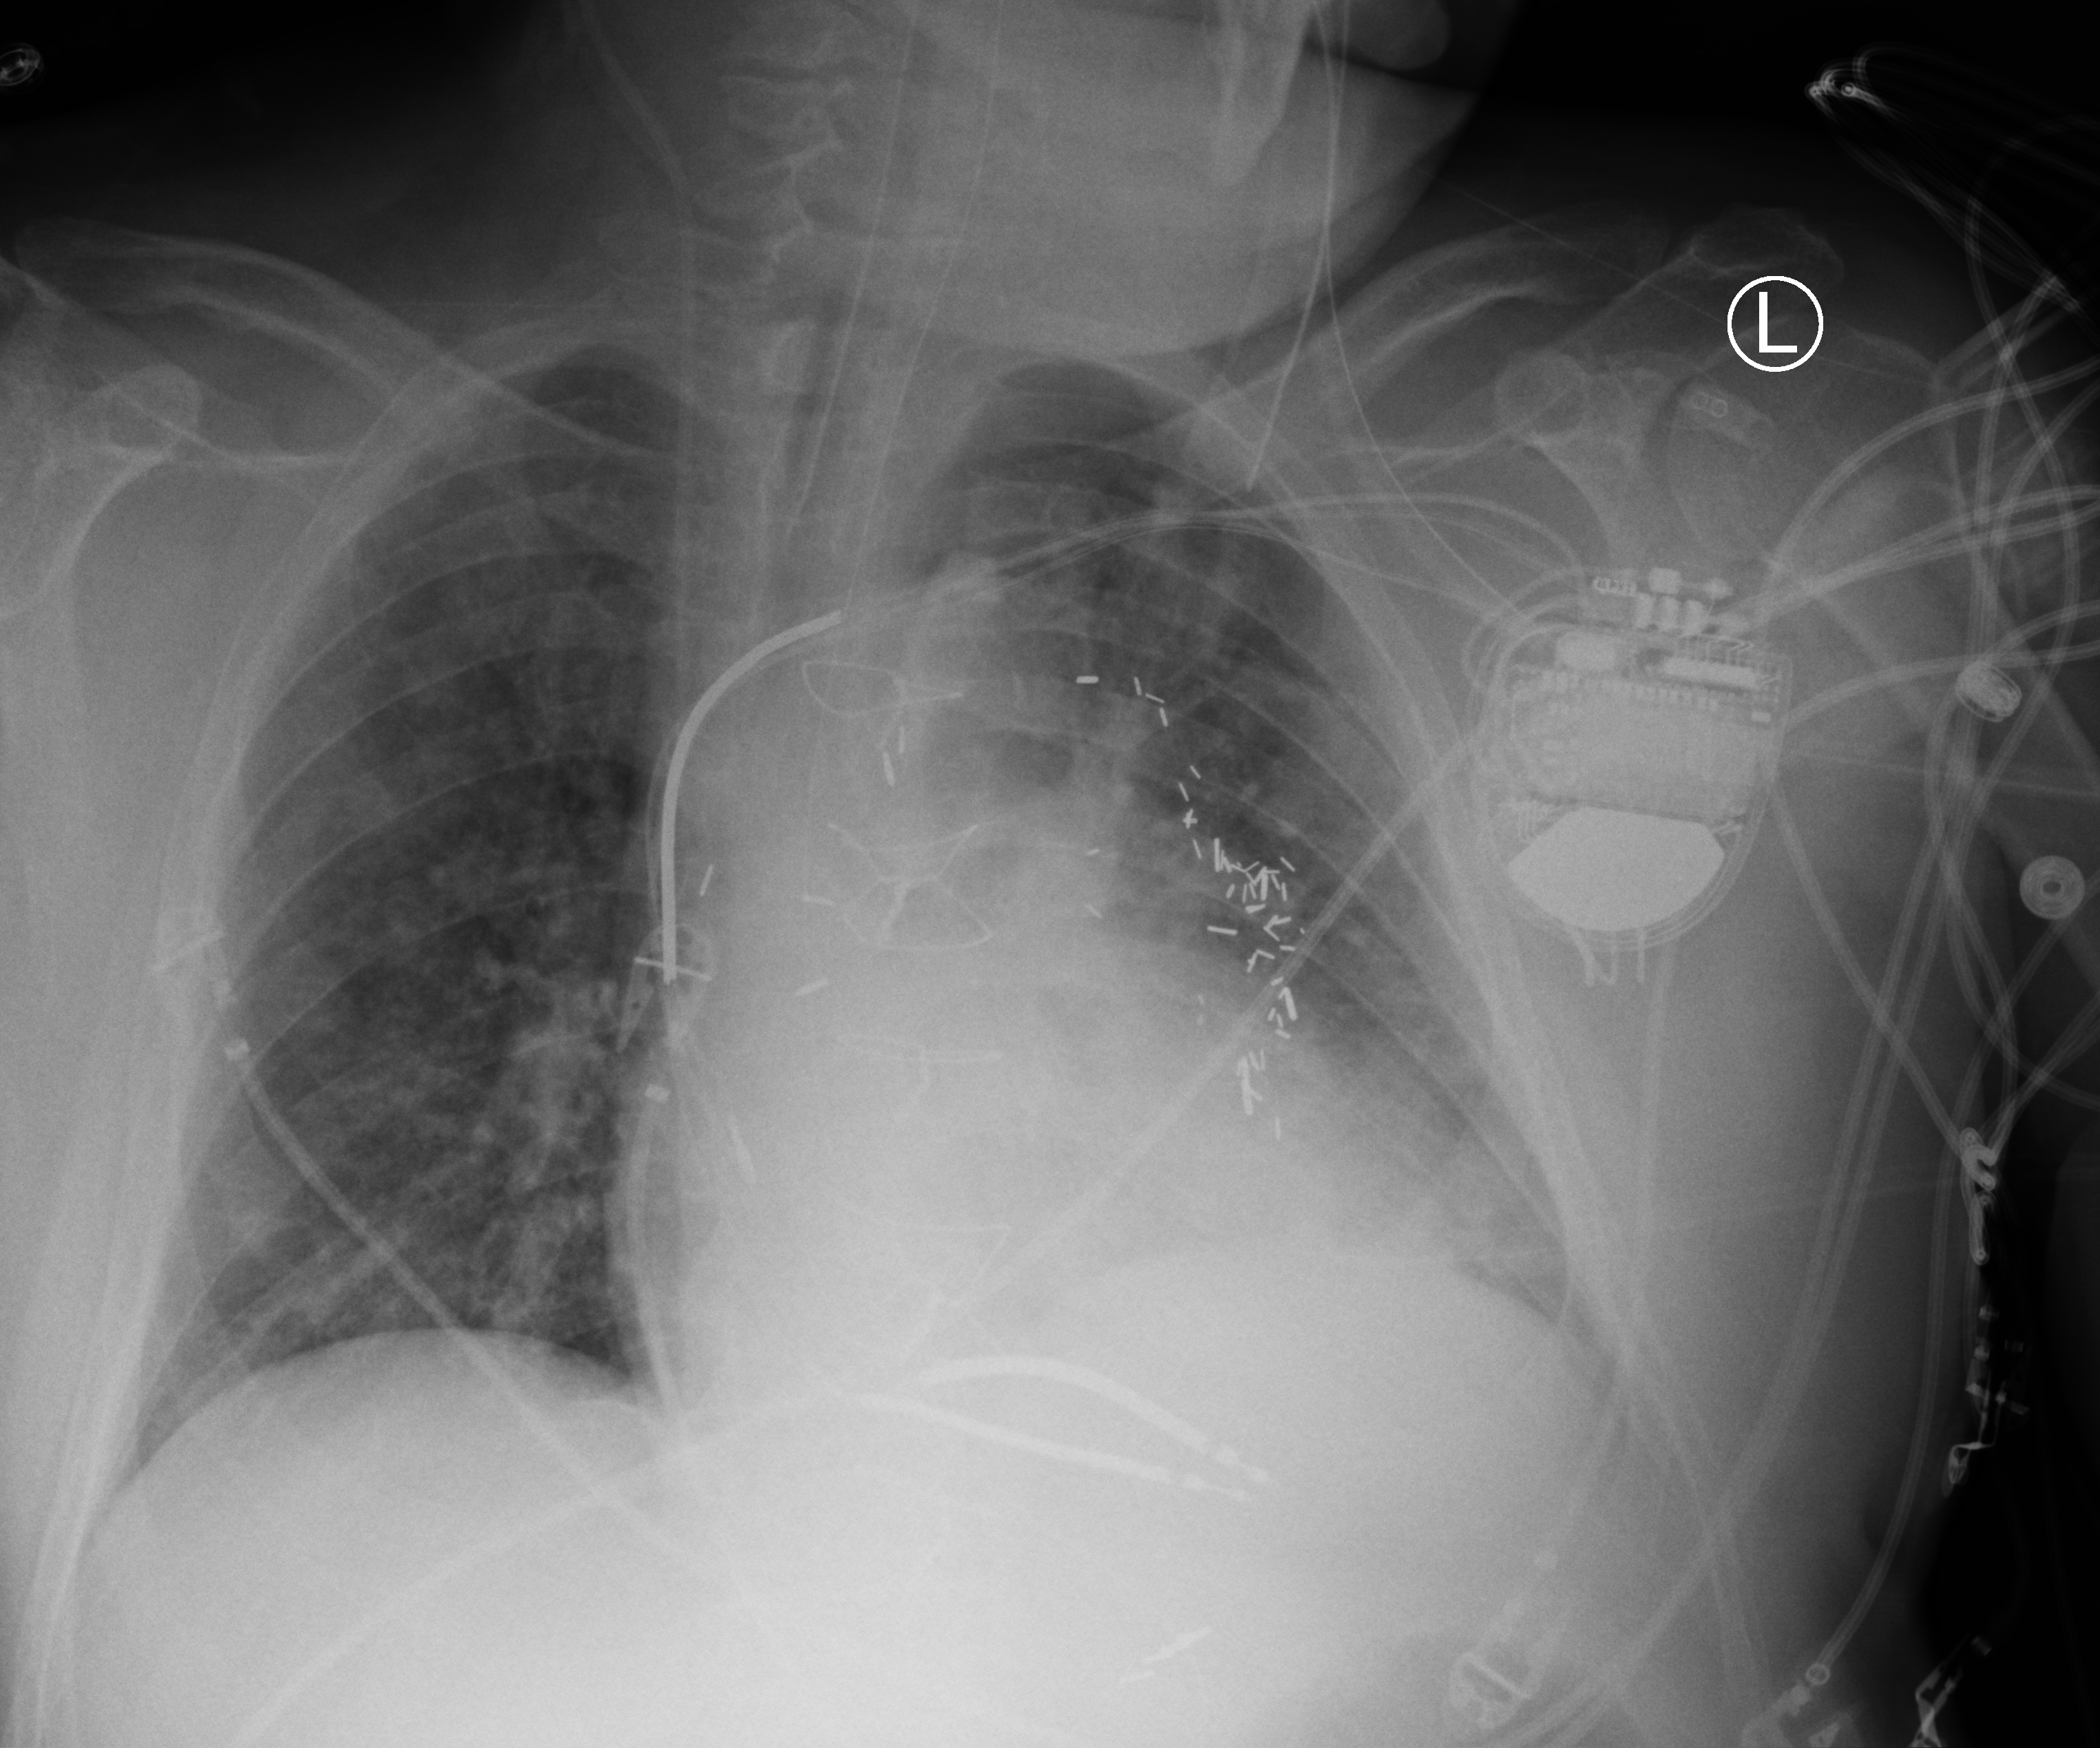
Portable chest radiograph, anteroposterior (AP) projection. Patient hospitalised with COVID-19; male, aged 60–74 years.
From the hospital-stay record, not from the radiograph (when in the stay this image was taken is not recorded):
- admitted to intensive care during this hospital stay: yes